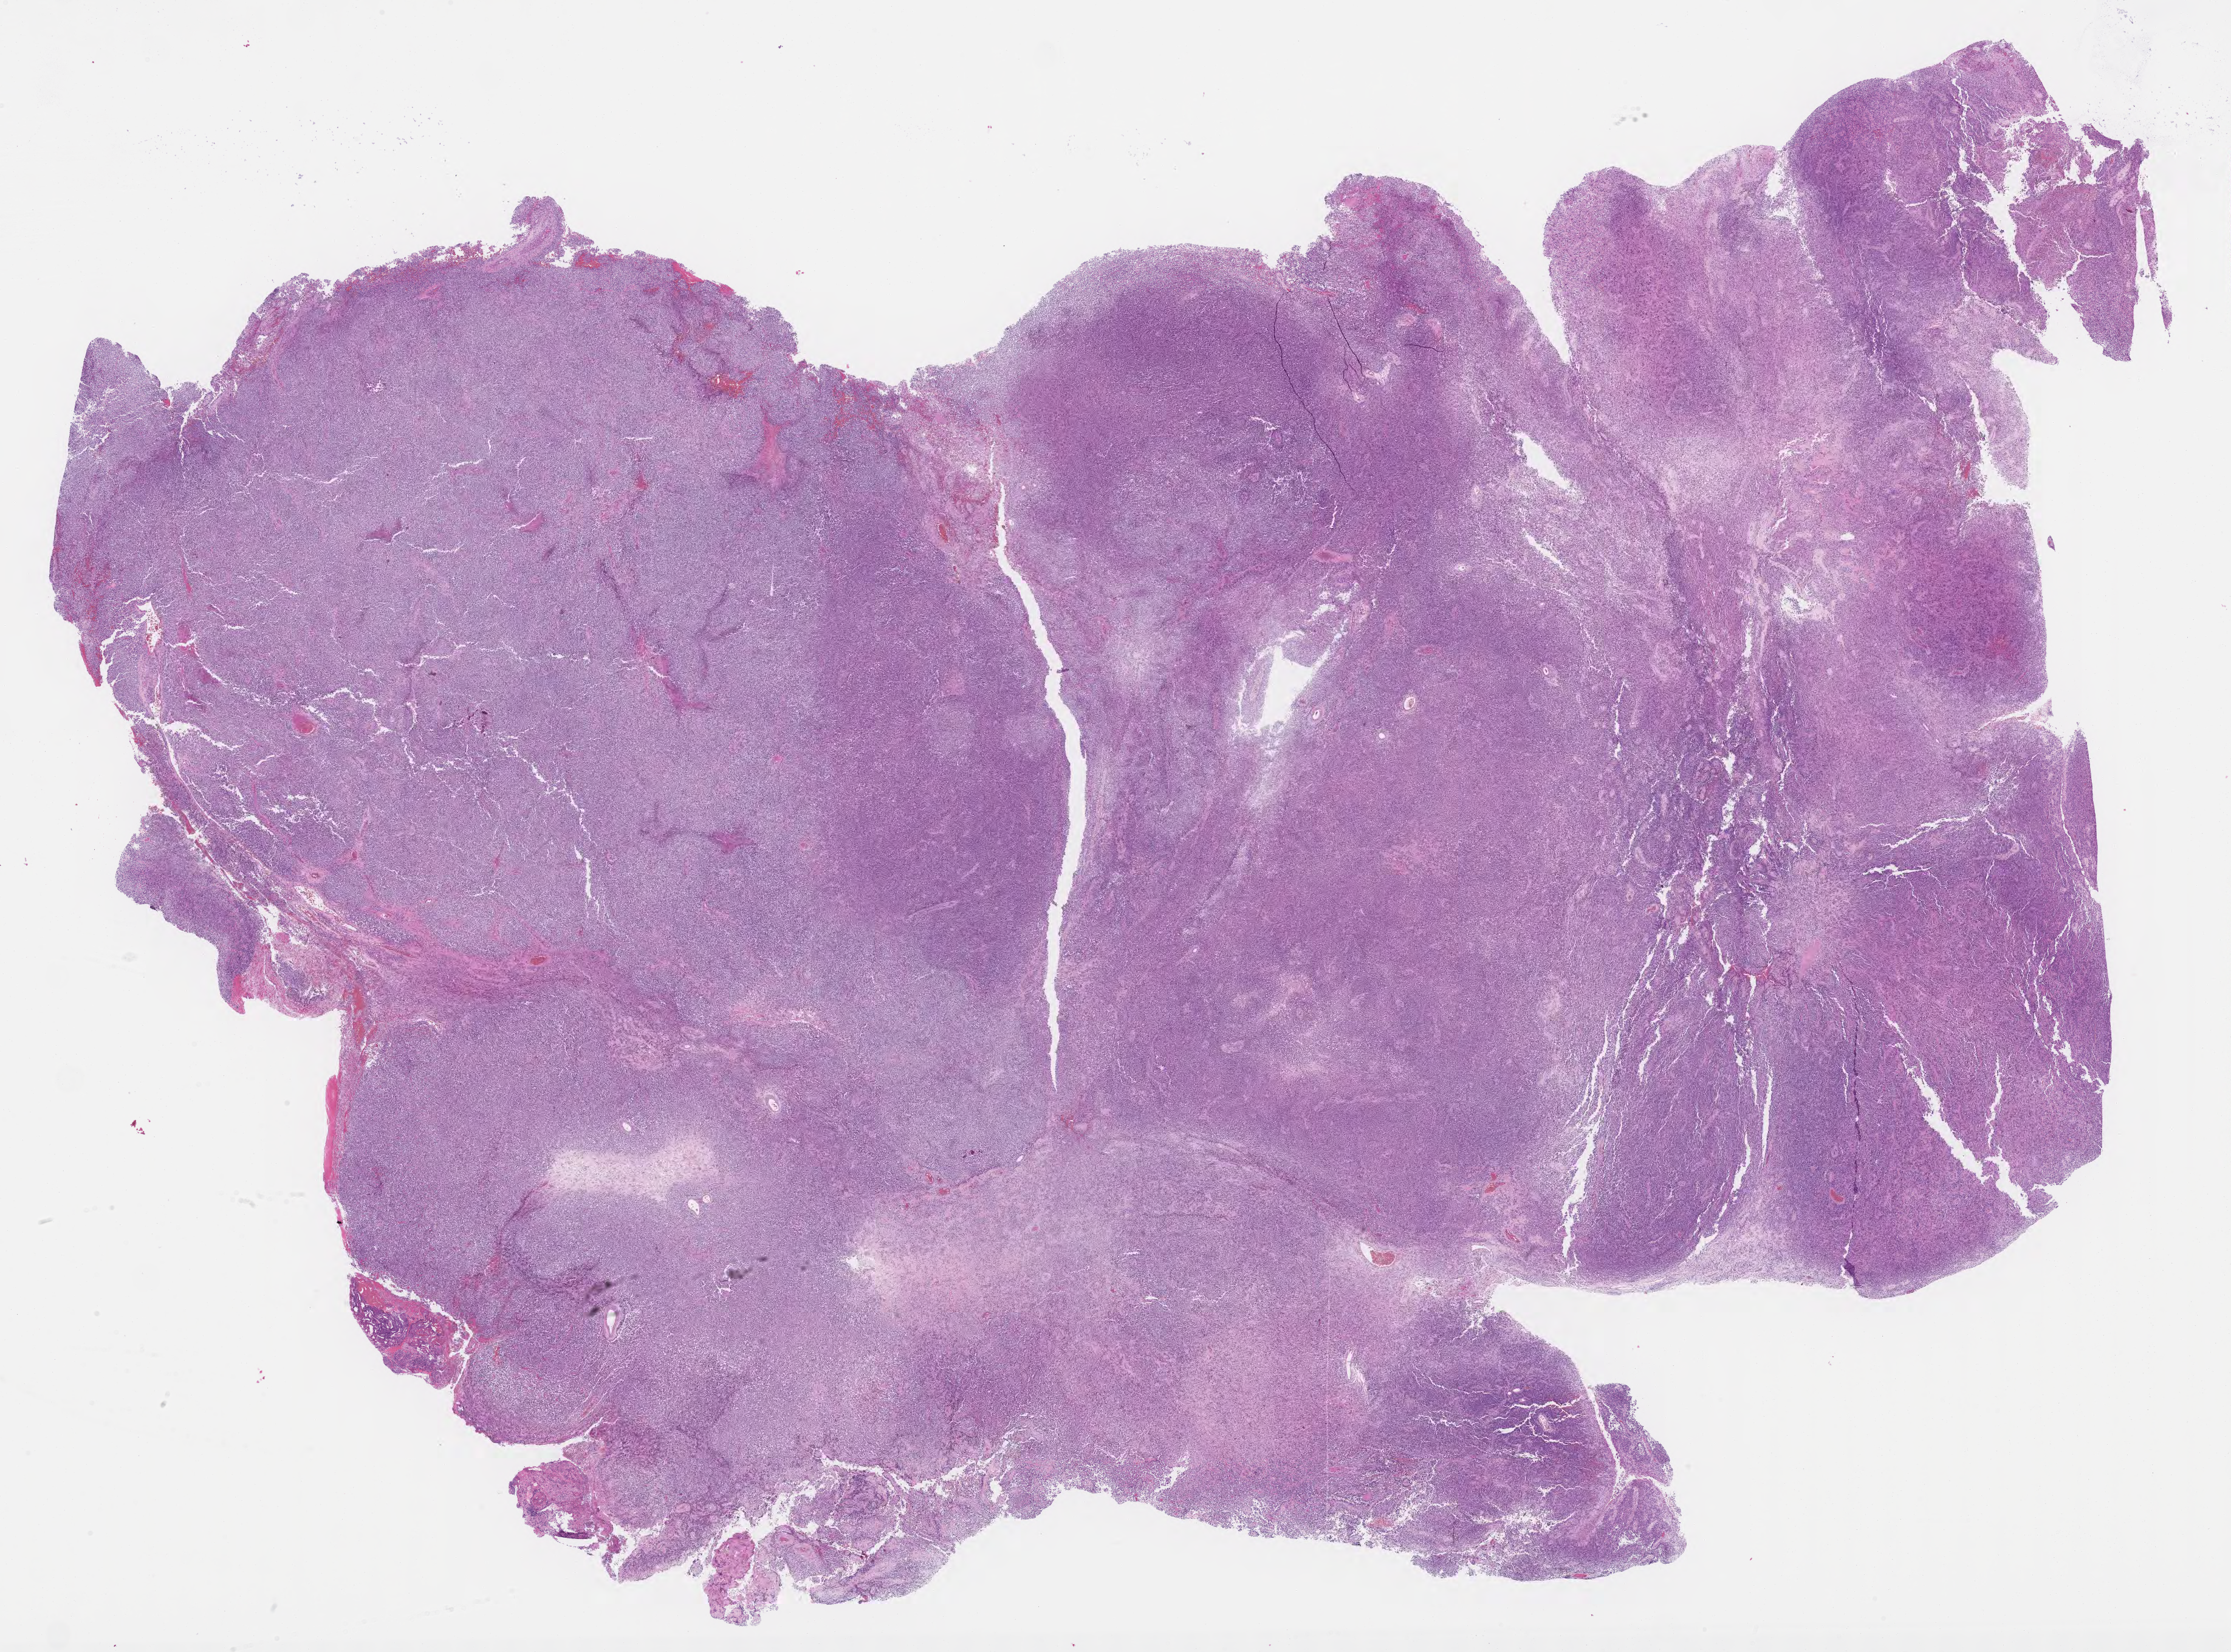
H&E whole-slide image of tumor tissue from the brain — low-resolution overview of the scanned area, about 29.7 x 22.0 mm, FFPE section. Female patient, age 123 months (10 years 3 months).
Recorded diagnosis: Glioma, malignant.